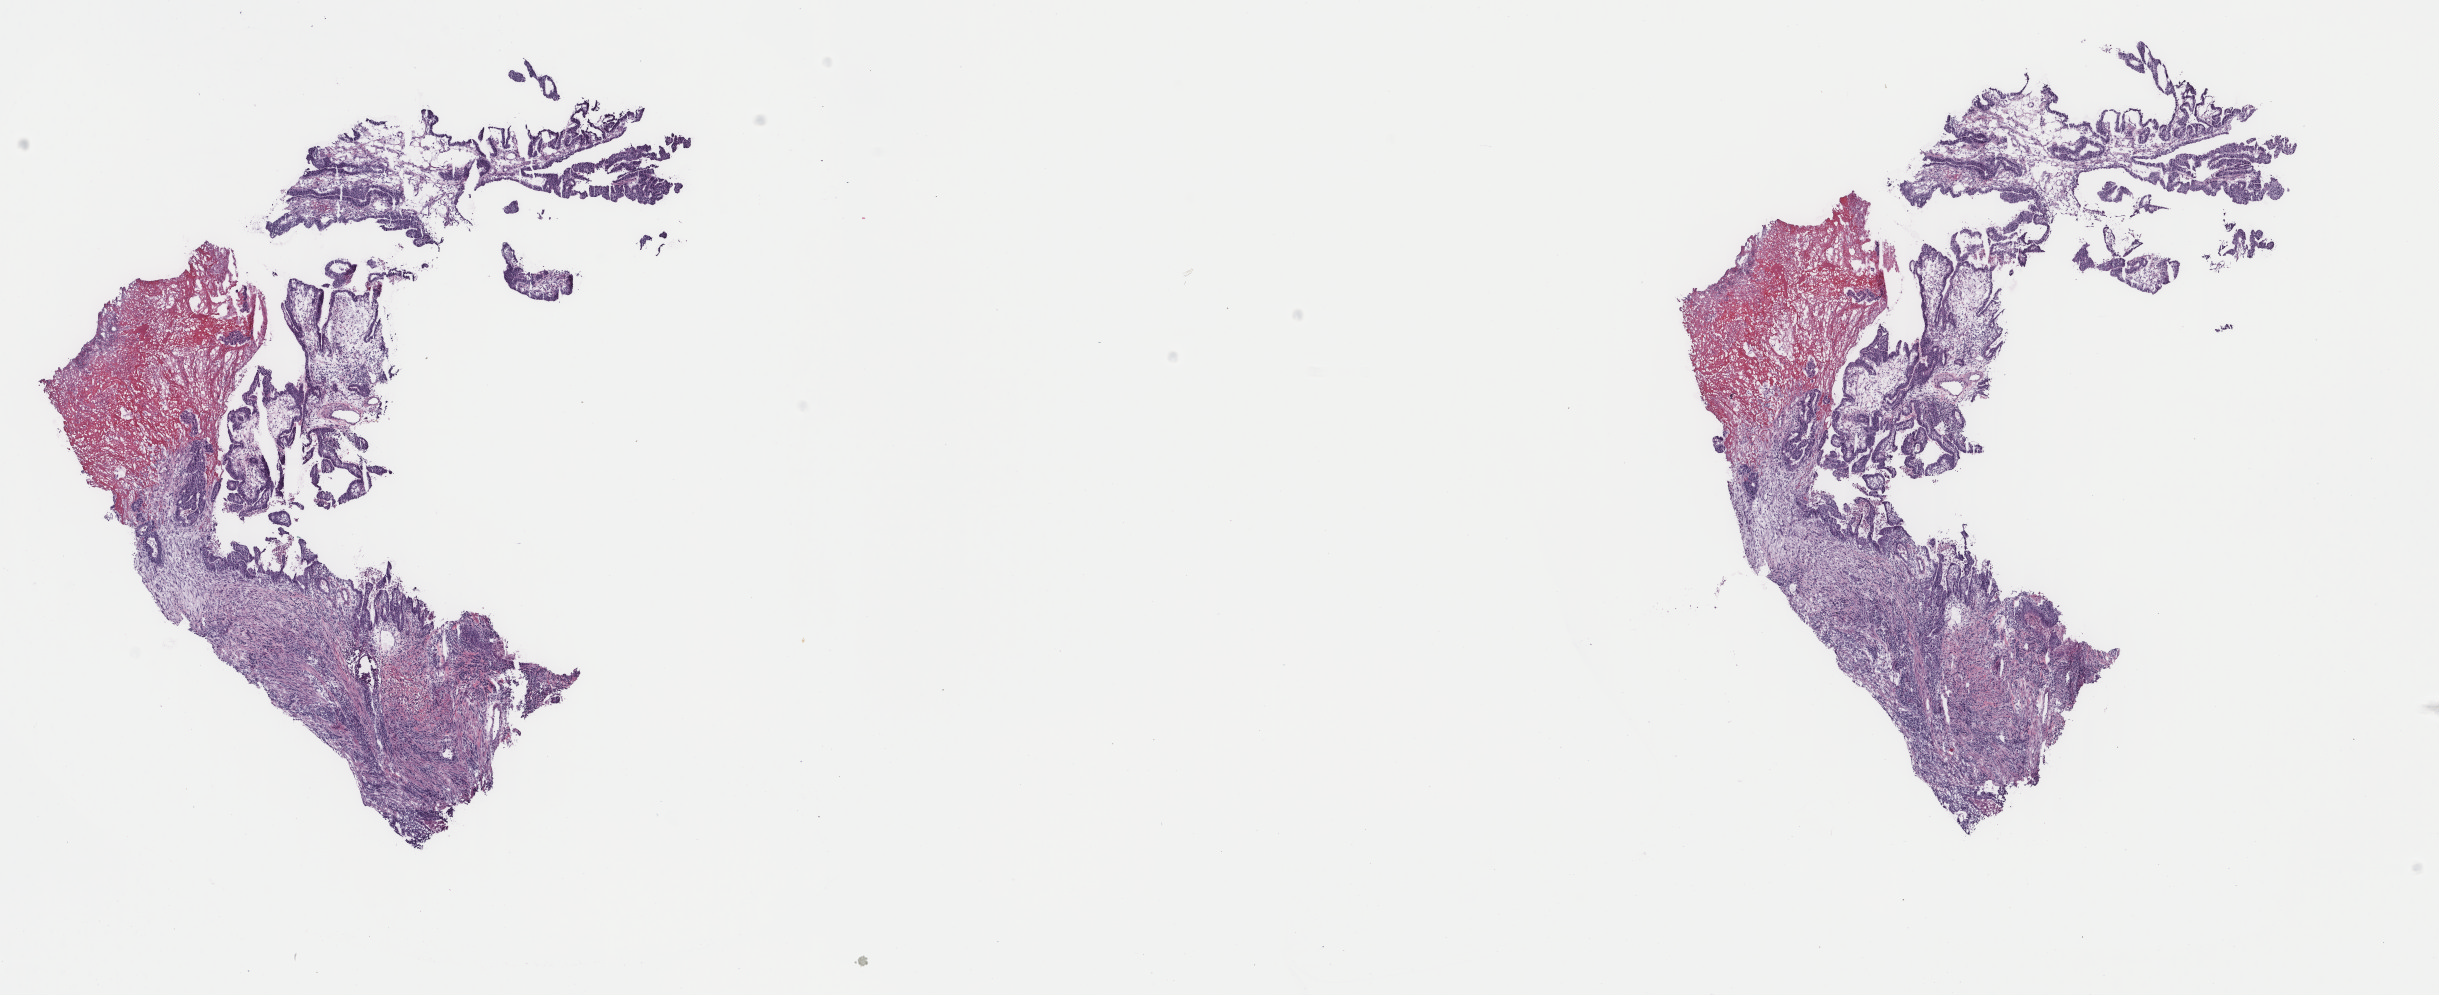
H&E-stained whole-slide image — a low-resolution overview of the entire scanned area, about 19.4 x 7.9 mm; frozen section; stomach, primary tumour sample. Male, age 71 years at initial diagnosis. Histologic grade: GX (grade cannot be assessed). Slide review estimates, as recorded: tumour cells 30%, tumour nuclei 70%, normal cells 0%, stromal cells 55%, necrosis 15%. Inflammatory infiltration, as recorded: lymphocyte infiltration 8%, monocyte infiltration 3%, neutrophil infiltration 1%.
TNM: T2 N0 M0. Diagnosis: Papillary adenocarcinoma, NOS (fundus of stomach). AJCC pathologic stage: IB.